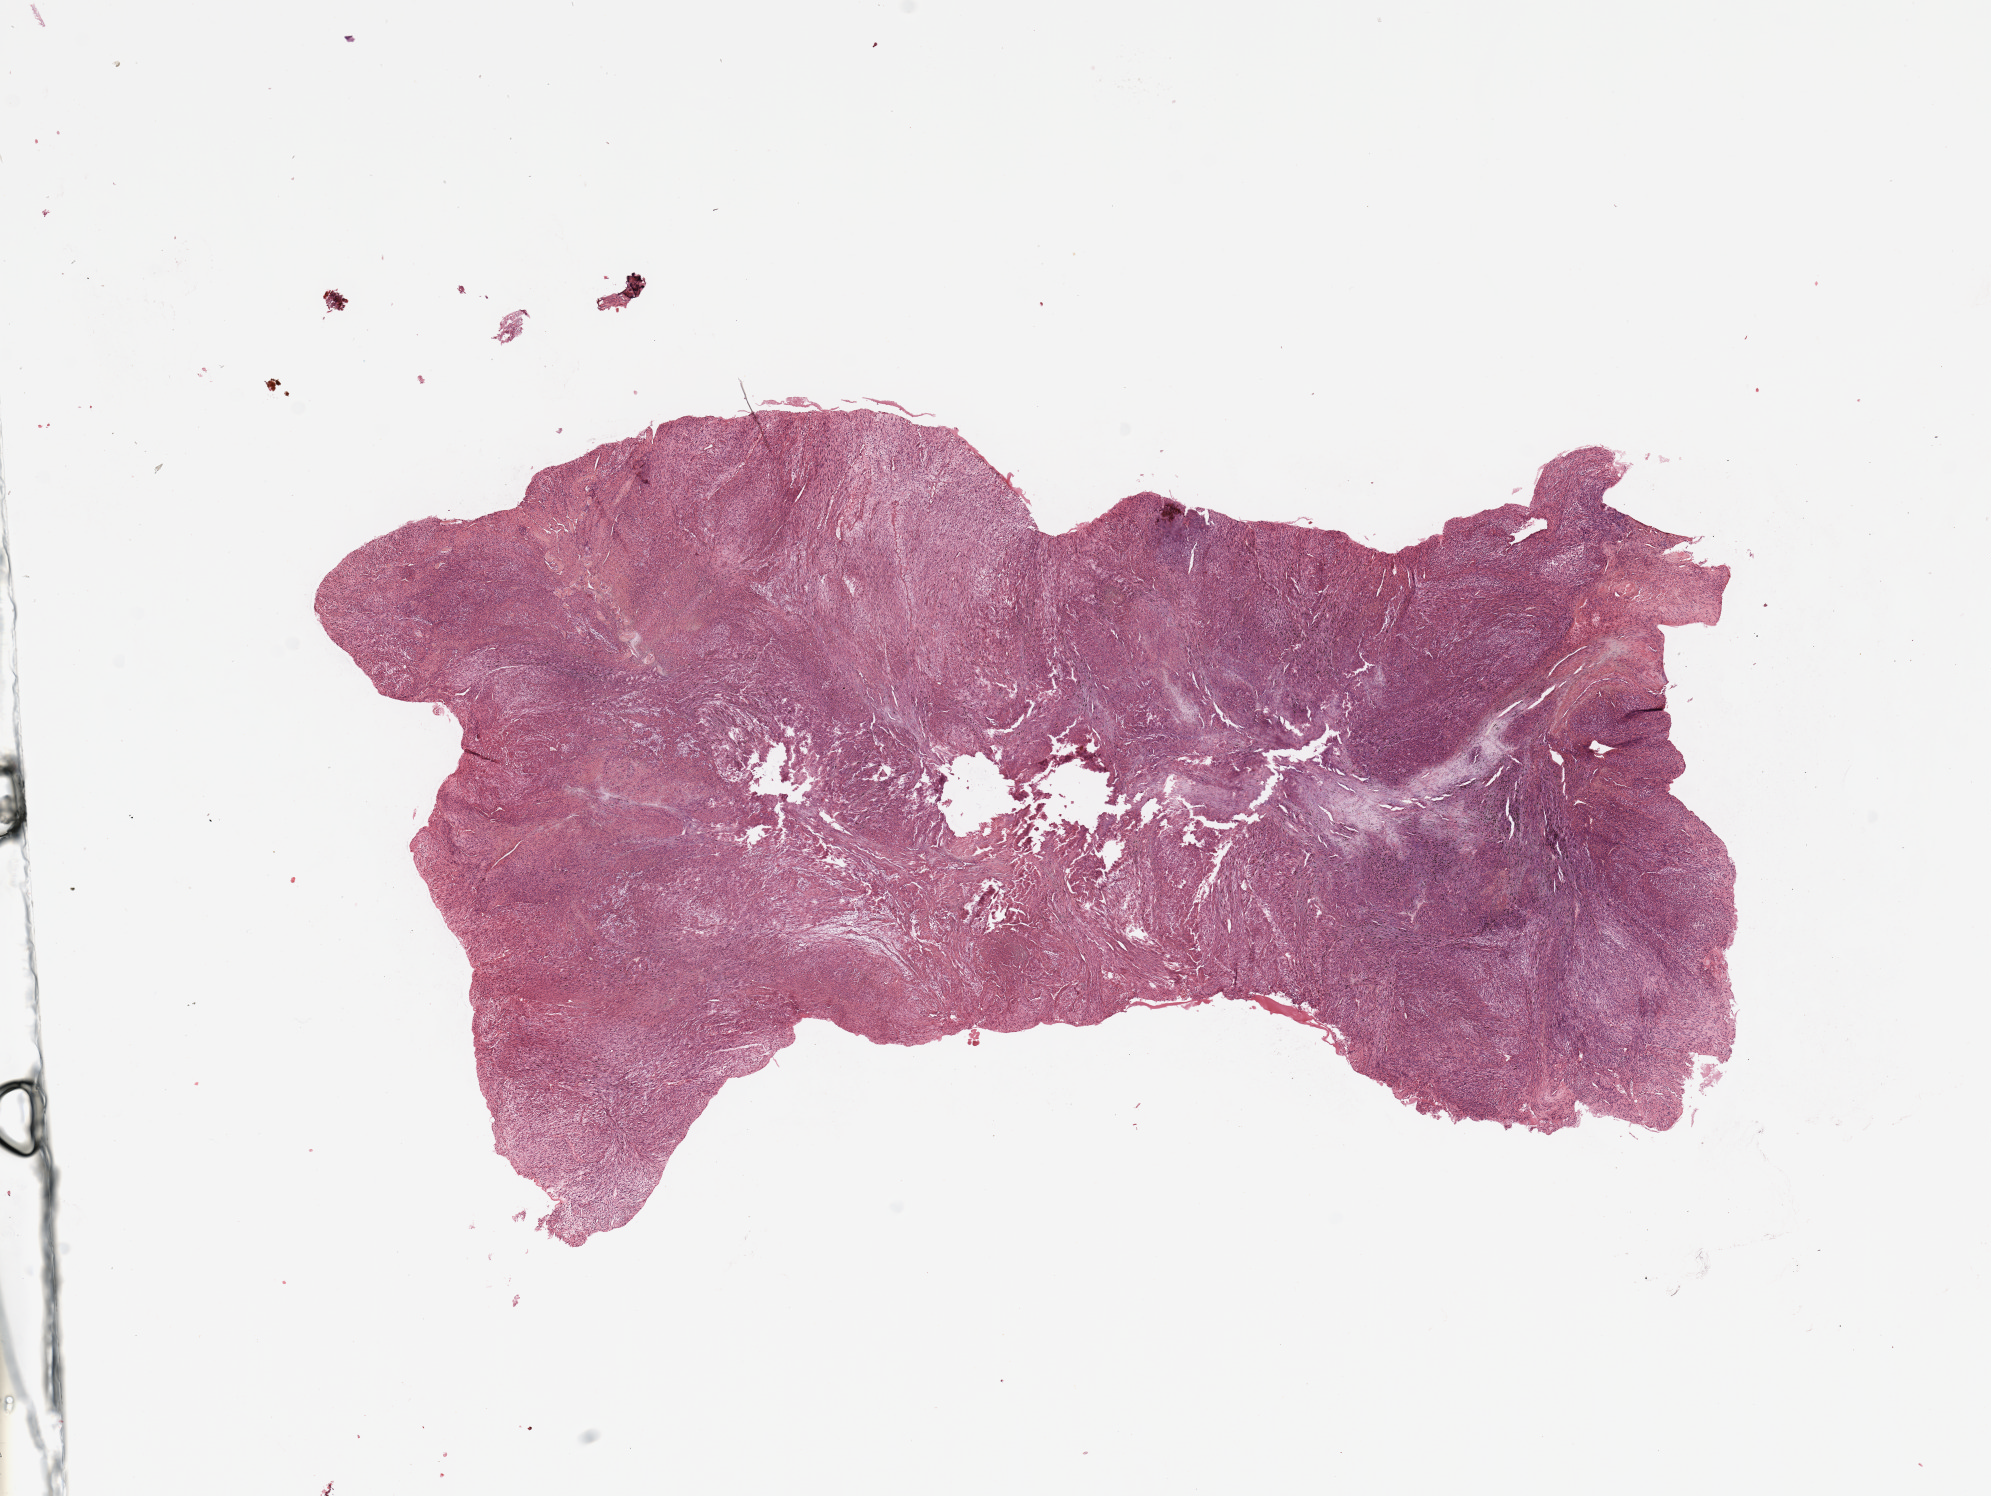
Whole-slide histology image, Hematoxylin and eosin (H&E) stained, low-resolution overview of the scanned area, about 15.8 x 11.8 mm (acquisition: 20x scan). Tumour tissue sample. Male, 66 y/o.
Patient diagnosis (cohort enrolment): sarcoma (site not recorded at cohort level). Primary tumour site (as recorded): chest.